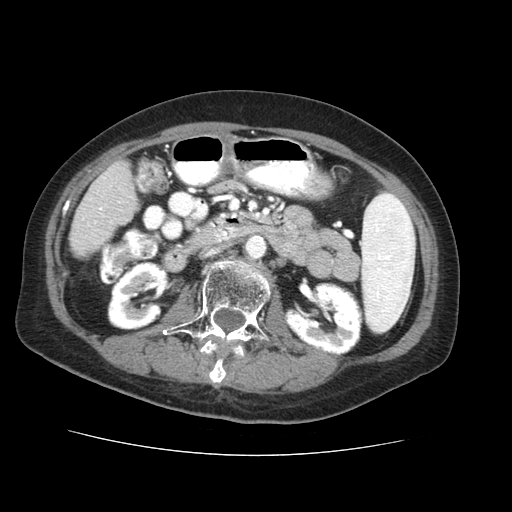
Contrast-enhanced abdominal CT (liver protocol), one axial slice; position 10 of 73 along the scan axis; soft-tissue window (W 400 / L 40 HU); 2.5 mm slice thickness; 512 × 512 image matrix, field of view 360 × 360 mm. From the clinical record (not read from this slice): diagnosis: hepatocellular carcinoma (patient treated with transarterial chemoembolisation; whether this scan precedes or follows treatment is not stated here); TNM stage (as recorded): Stage-IVB; Child-Pugh class: A; tumour differentiation: well differentiated; tumour nodularity: uninodular.
Structures marked on this image (semi-automatically segmented with operator editing):
- liver parenchyma outside the tumour (the mass and vessels are separate outlines, so this box may not span the whole liver): box from (x=70, y=162) to (x=136, y=256) px
- liver vessels: (x=103, y=173)–(x=108, y=179)